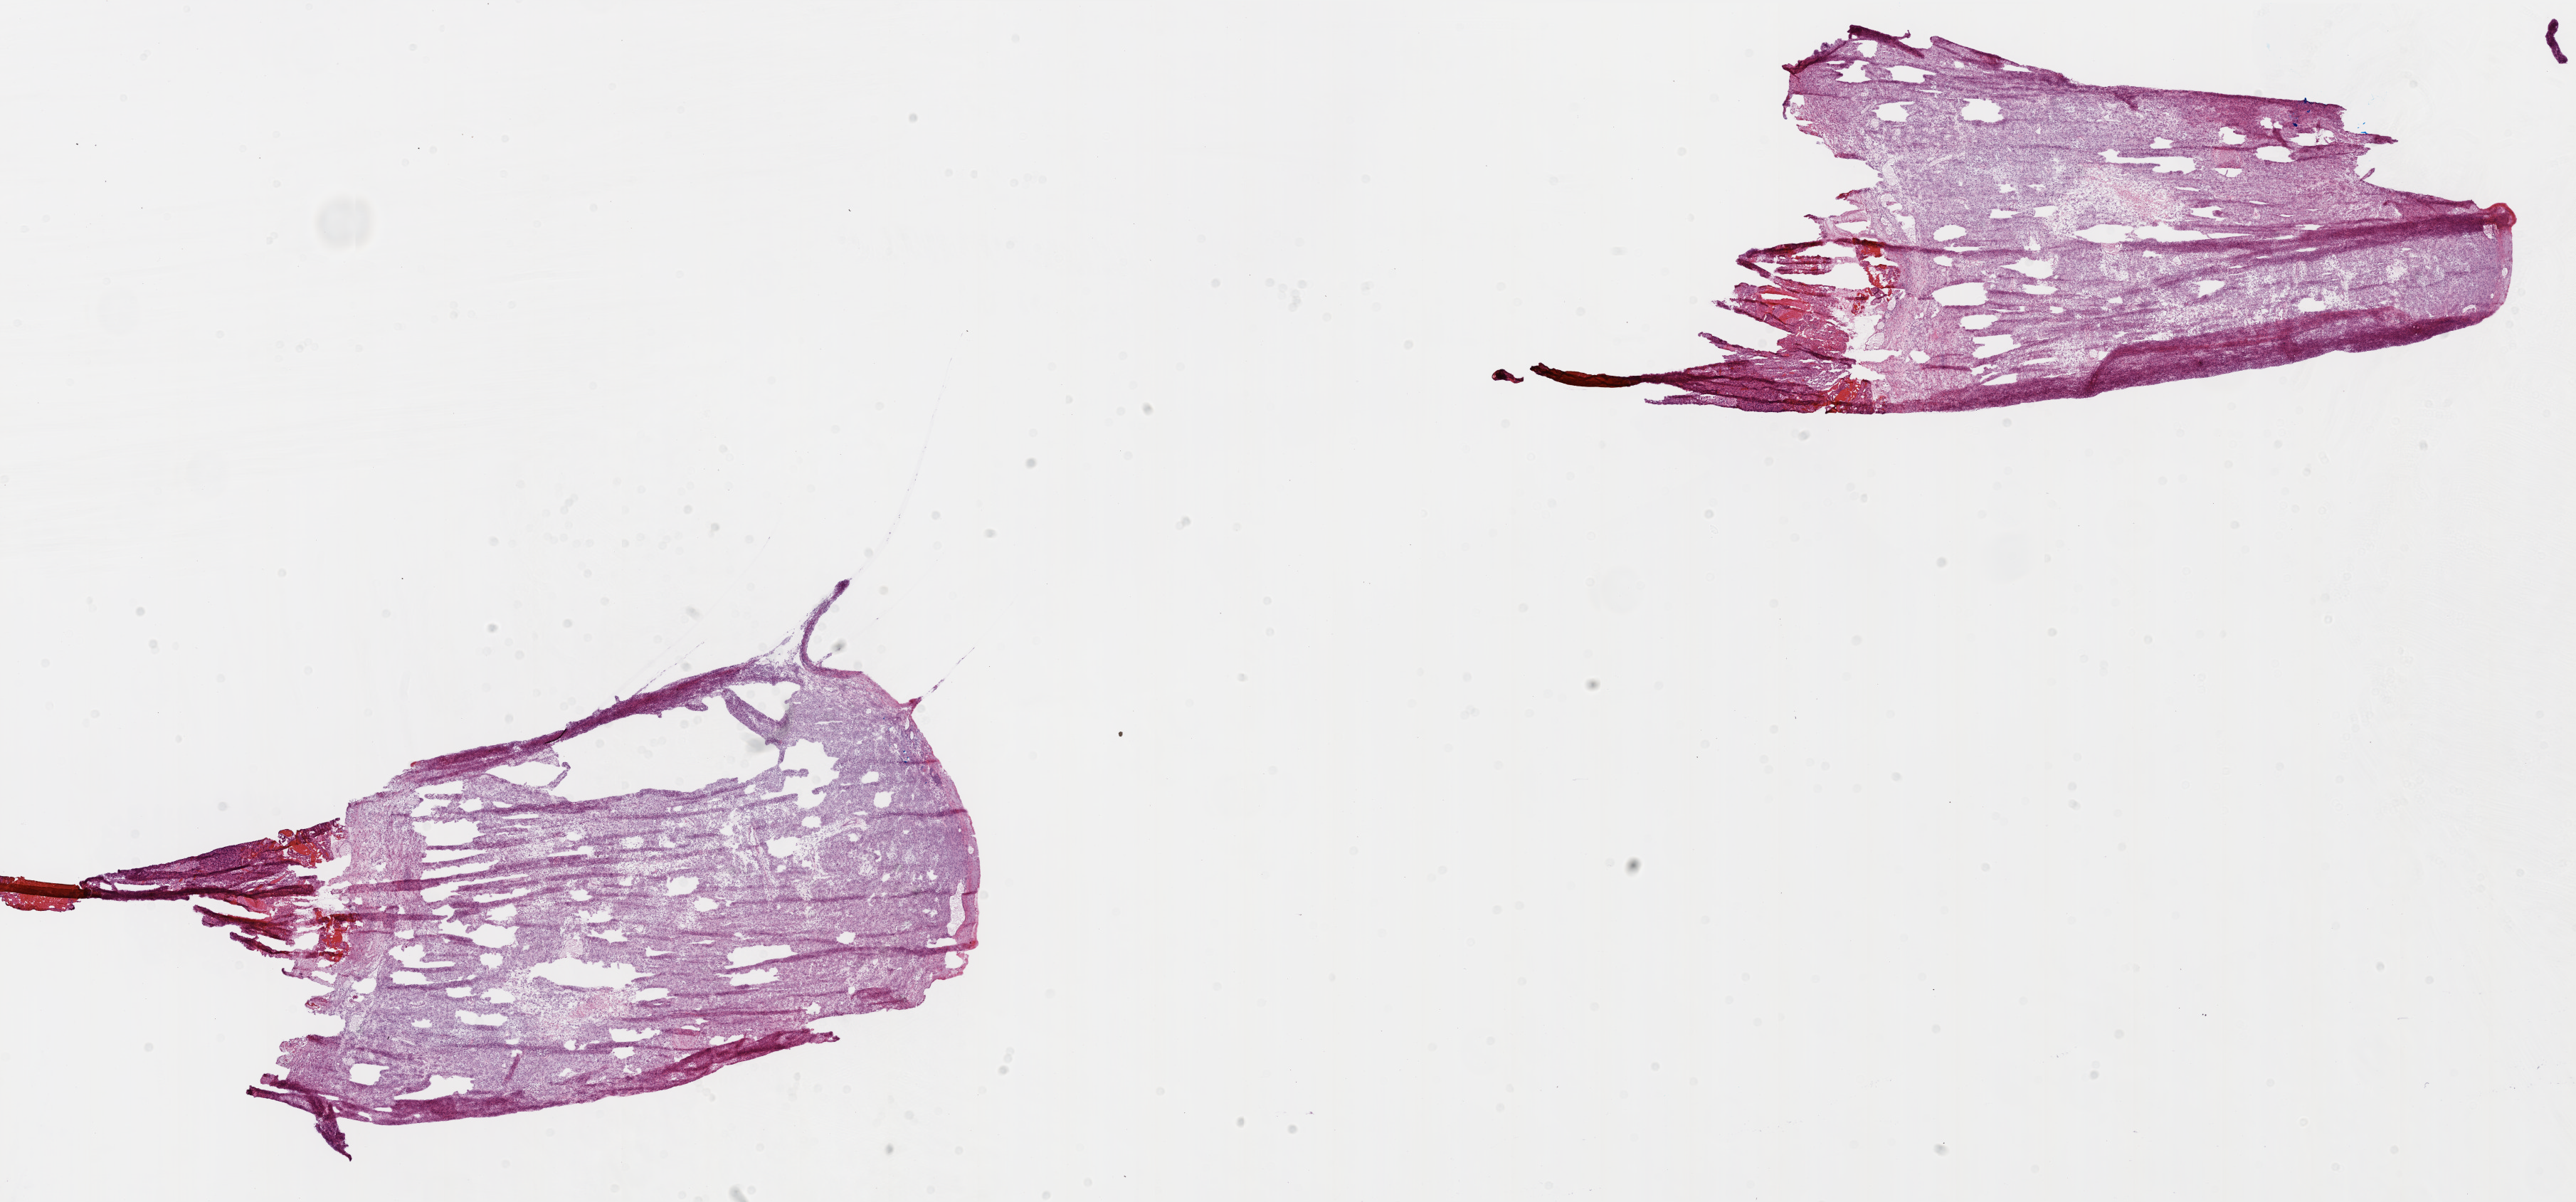
Whole-slide histology image, H&E-stained, shown as a low-resolution overview of the whole scanned area (about 29.0 x 13.5 mm, from a 20x scan); frozen section; brain, primary tumour sample. Male, age 54 years at initial diagnosis.
Histologic diagnosis: Glioblastoma.